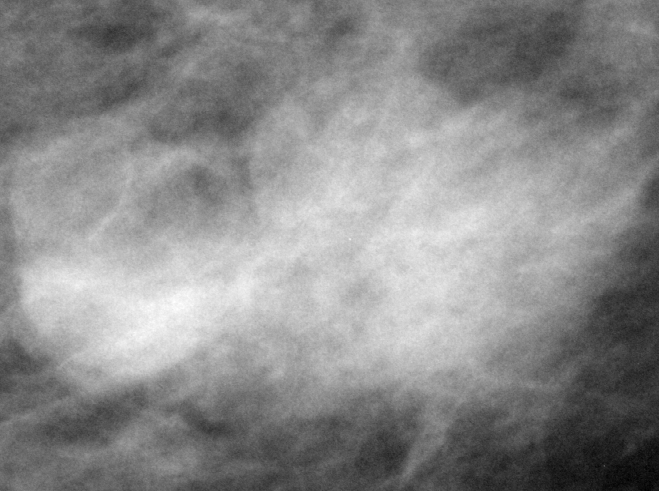
Cropped region of a digitized screen-film mammogram centred on a radiologist-marked abnormality; right breast; MLO view.
- Finding: mass, shape lobulated, margins obscured; BI-RADS assessment category 4; pathology result (as recorded, not read from the image): benign.